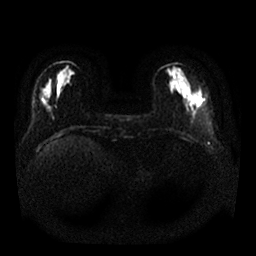
Breast MRI, one axial slice; slice 7 of 25 in the series (ordered by position); diffusion-weighted series; image 2 of 4 stored at this slice position (different b-values; order by instance number); 1.5 T; 4 mm slice thickness; 256 × 256 image matrix, field of view 340 × 340 mm. Female patient.
Structures marked on this image (manually delineated by an expert):
- tumour on diffusion-weighted imaging: bounding box (x1, y1, x2, y2) in pixels: (197, 86, 206, 105)